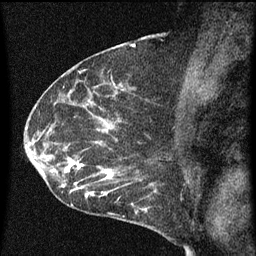
Breast MRI (dynamic contrast-enhanced), one sagittal slice; position 39 of 60 along the scan axis; dynamic contrast-enhanced series, image 2 of 3 at this slice position (ordered by acquisition); 1.5 T; TE 4.2 ms, TR 8 ms; 2 mm slice thickness; 256 × 256 image matrix, field of view 180 × 180 mm. Female patient, age 54 years.
Structures marked on this image (semi-automatic segmentation, software-assisted and operator-edited):
- analysis volume of interest (the breast-tissue region the enhancement analysis was run in; not a lesion): bounding box (x1, y1, x2, y2) in pixels: (49, 138, 164, 209)
- tumour enhancement mask (voxels above the 70 % enhancement threshold inside the analysis volume of interest): (49, 138, 155, 209)